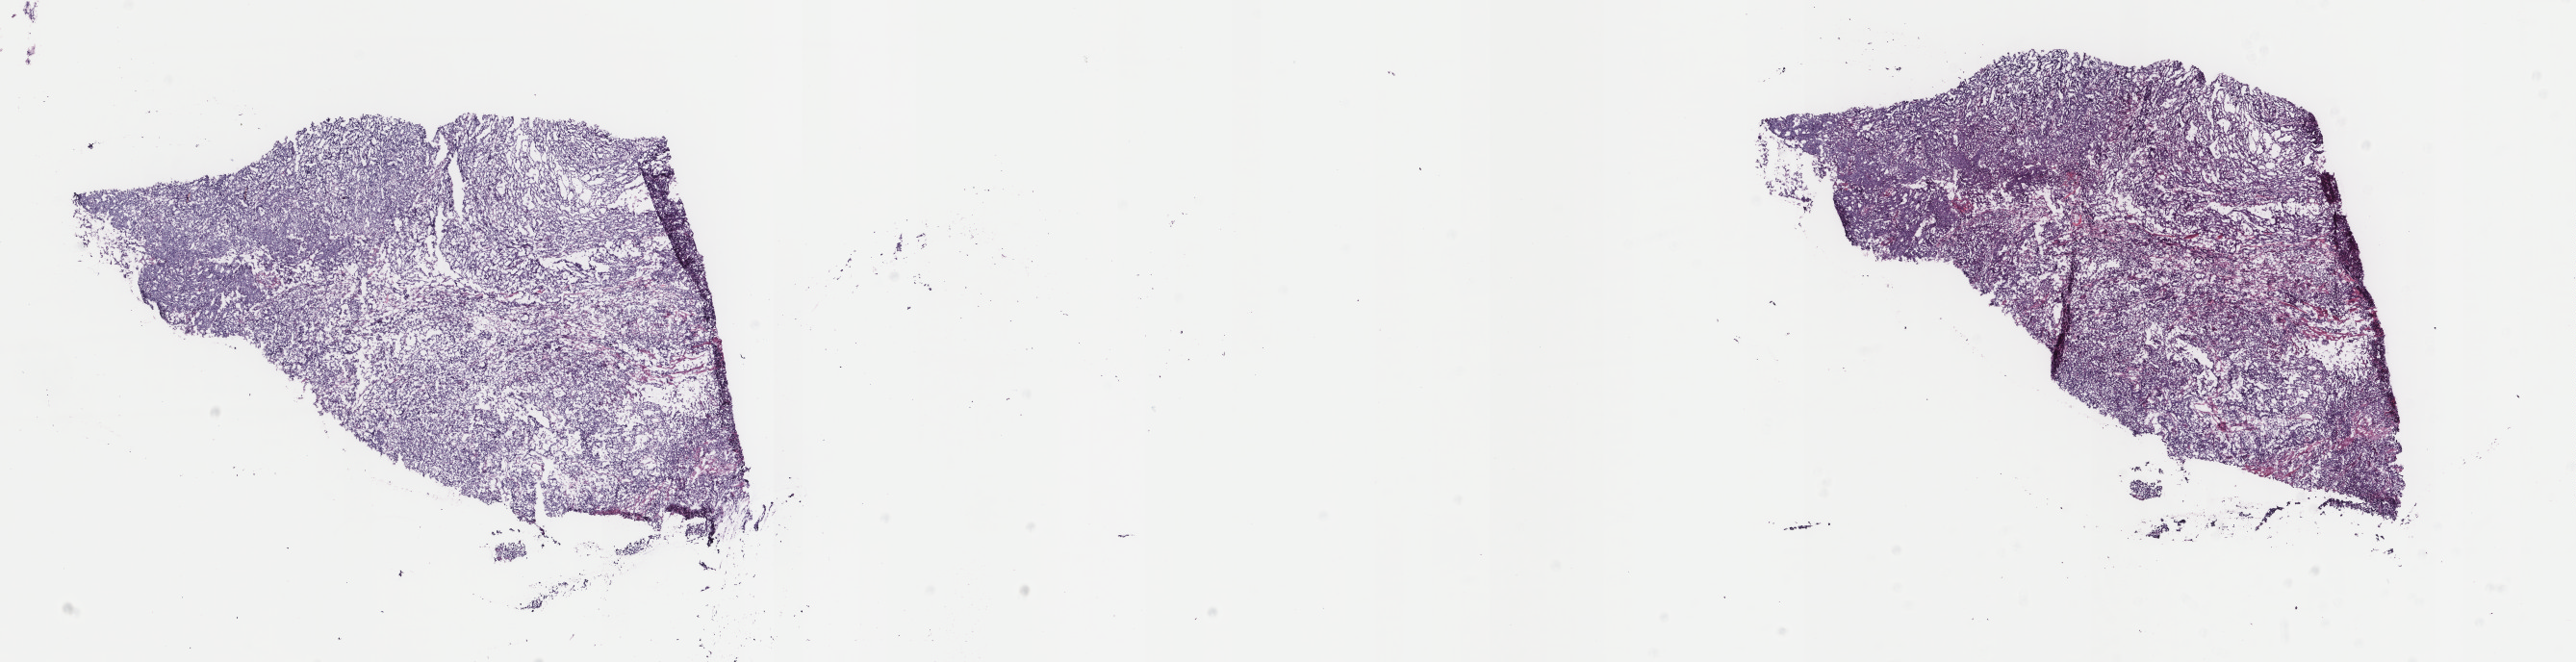
Digitized Hematoxylin and eosin (H&E) stained tissue section (whole slide), whole scanned area (about 21.2 x 5.5 mm, from a 40x scan) shown as a low-resolution overview; frozen section from the top of the tissue portion; uterus, primary tumour sample. Female patient; age at initial diagnosis 64 years.
Diagnosis: Endometrioid adenocarcinoma, NOS.